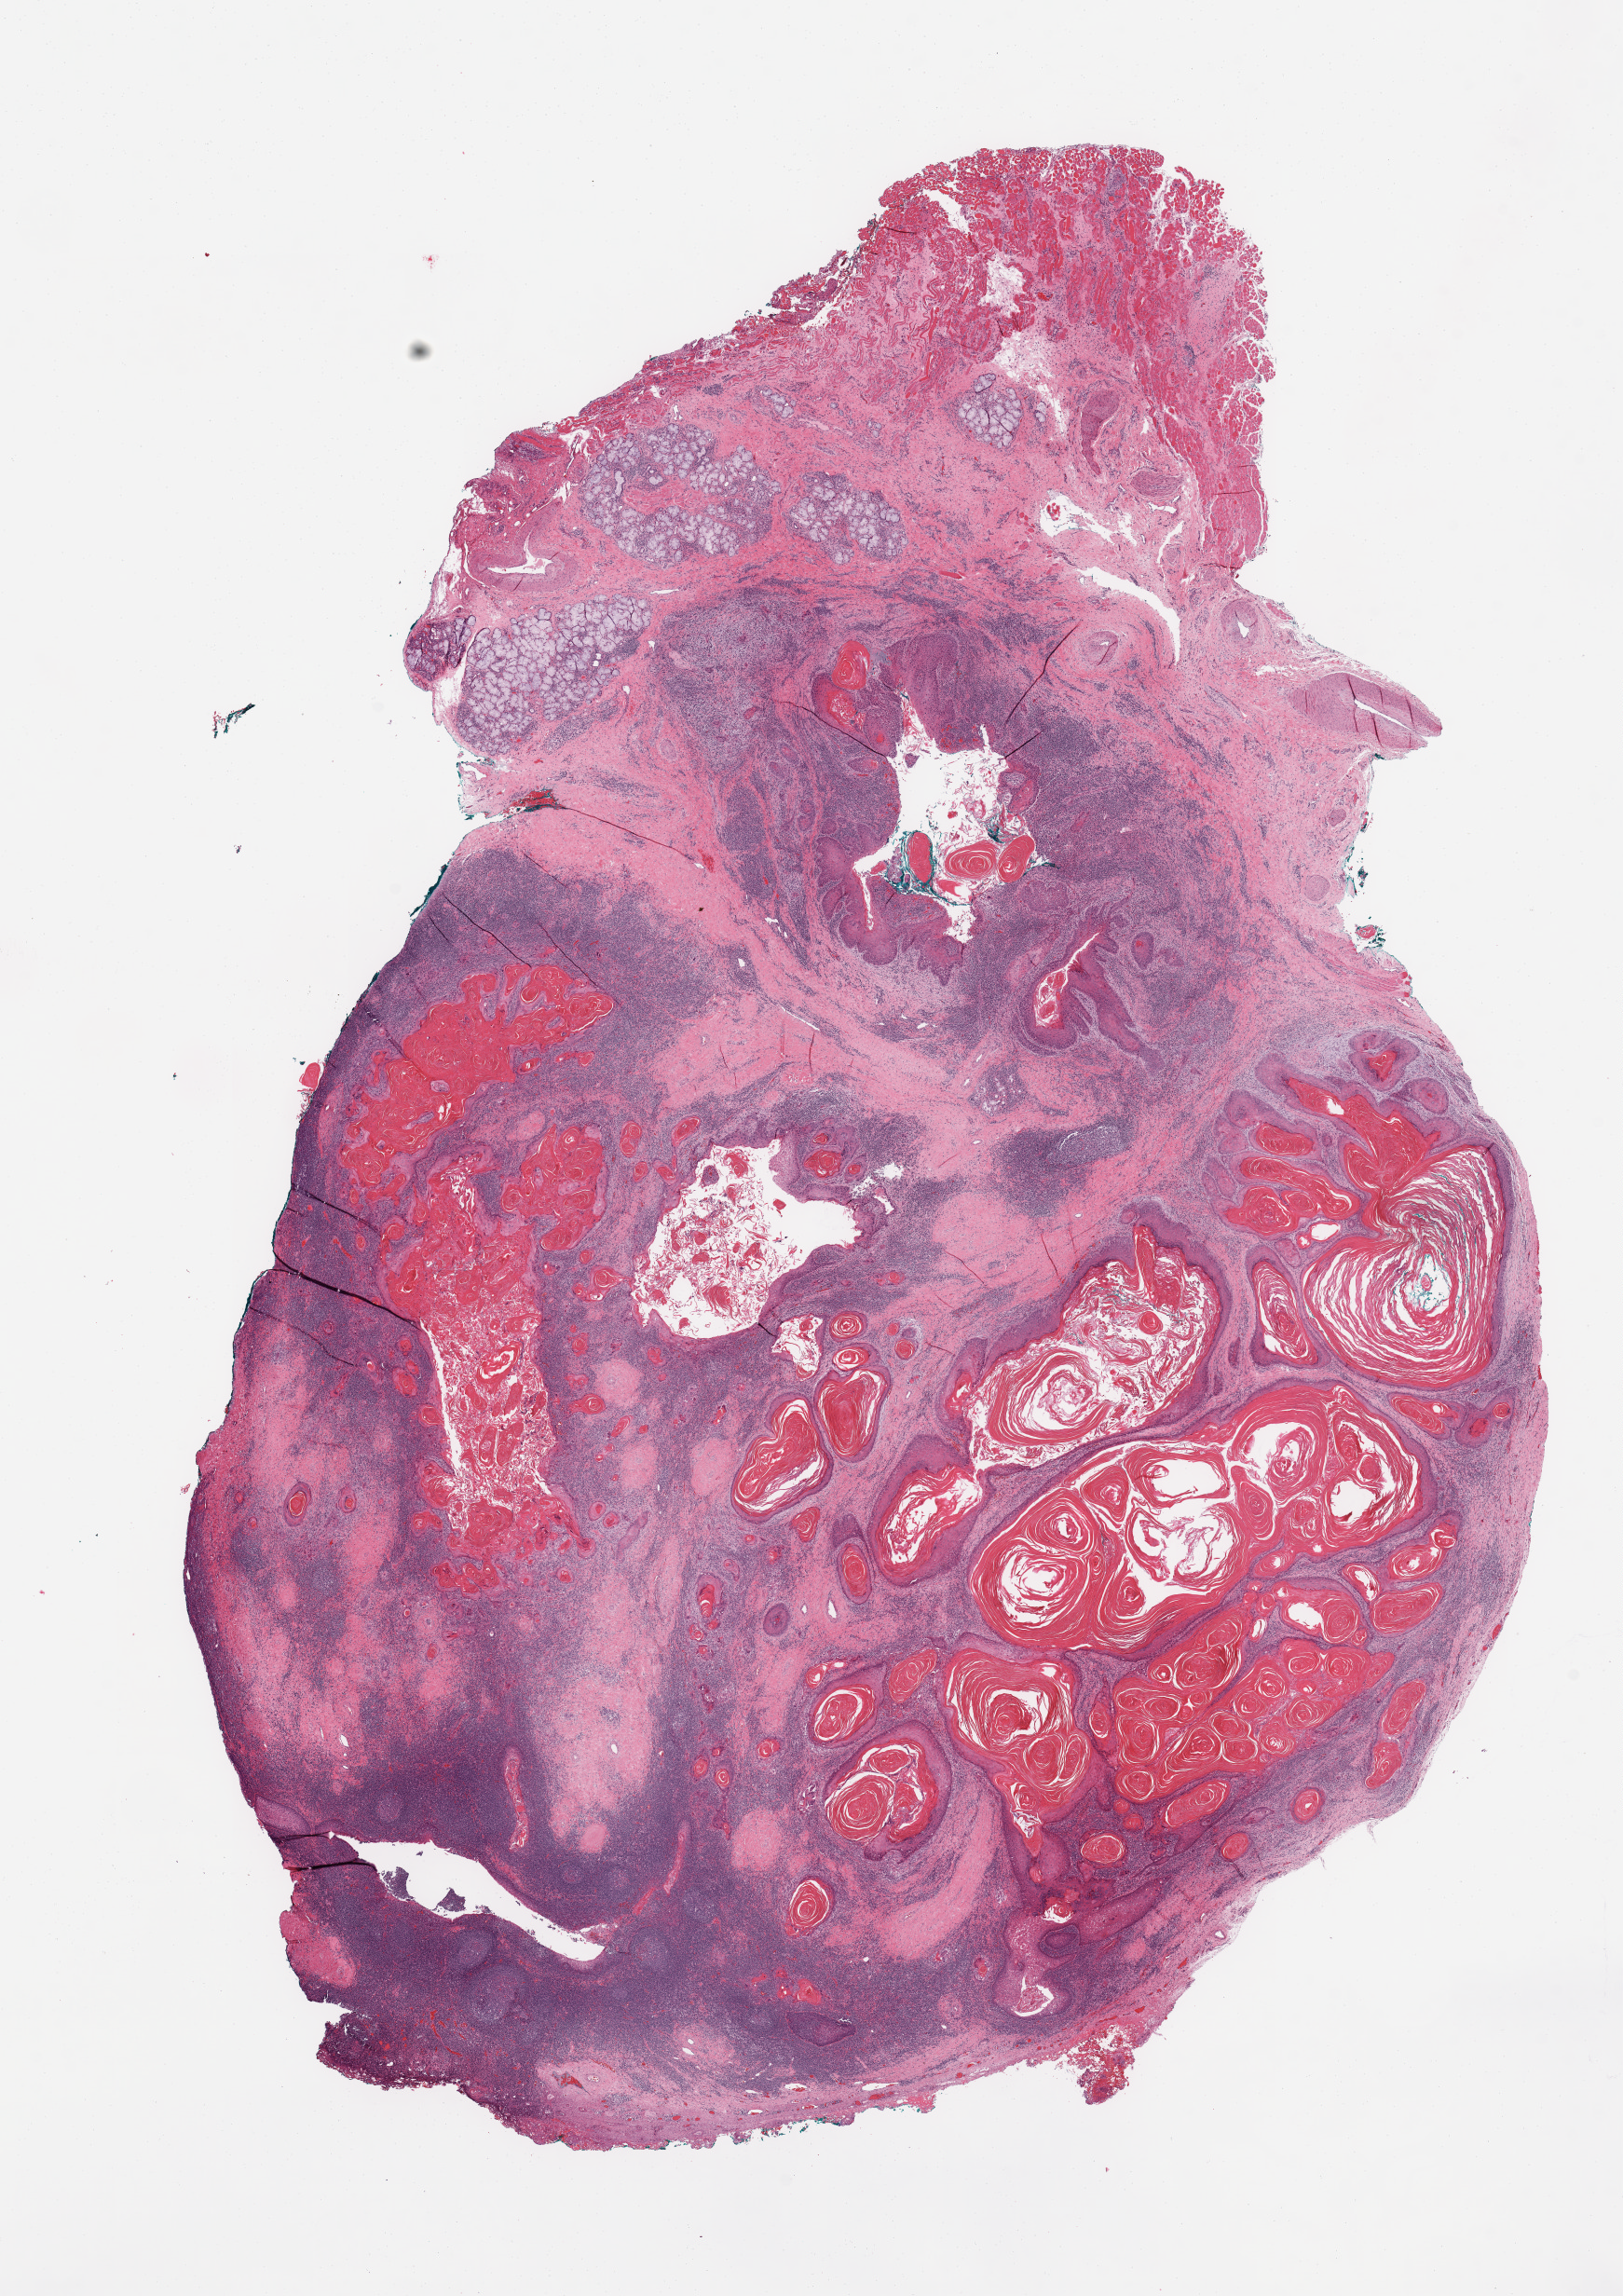
H&E whole-slide image — a low-resolution overview of the entire scanned area, about 13.8 x 19.5 mm (from a 20x scan), head and neck, tissue type not recorded. Male, 56 y/o.
Patient diagnosis: Squamous cell carcinoma, NOS (cheek mucosa).